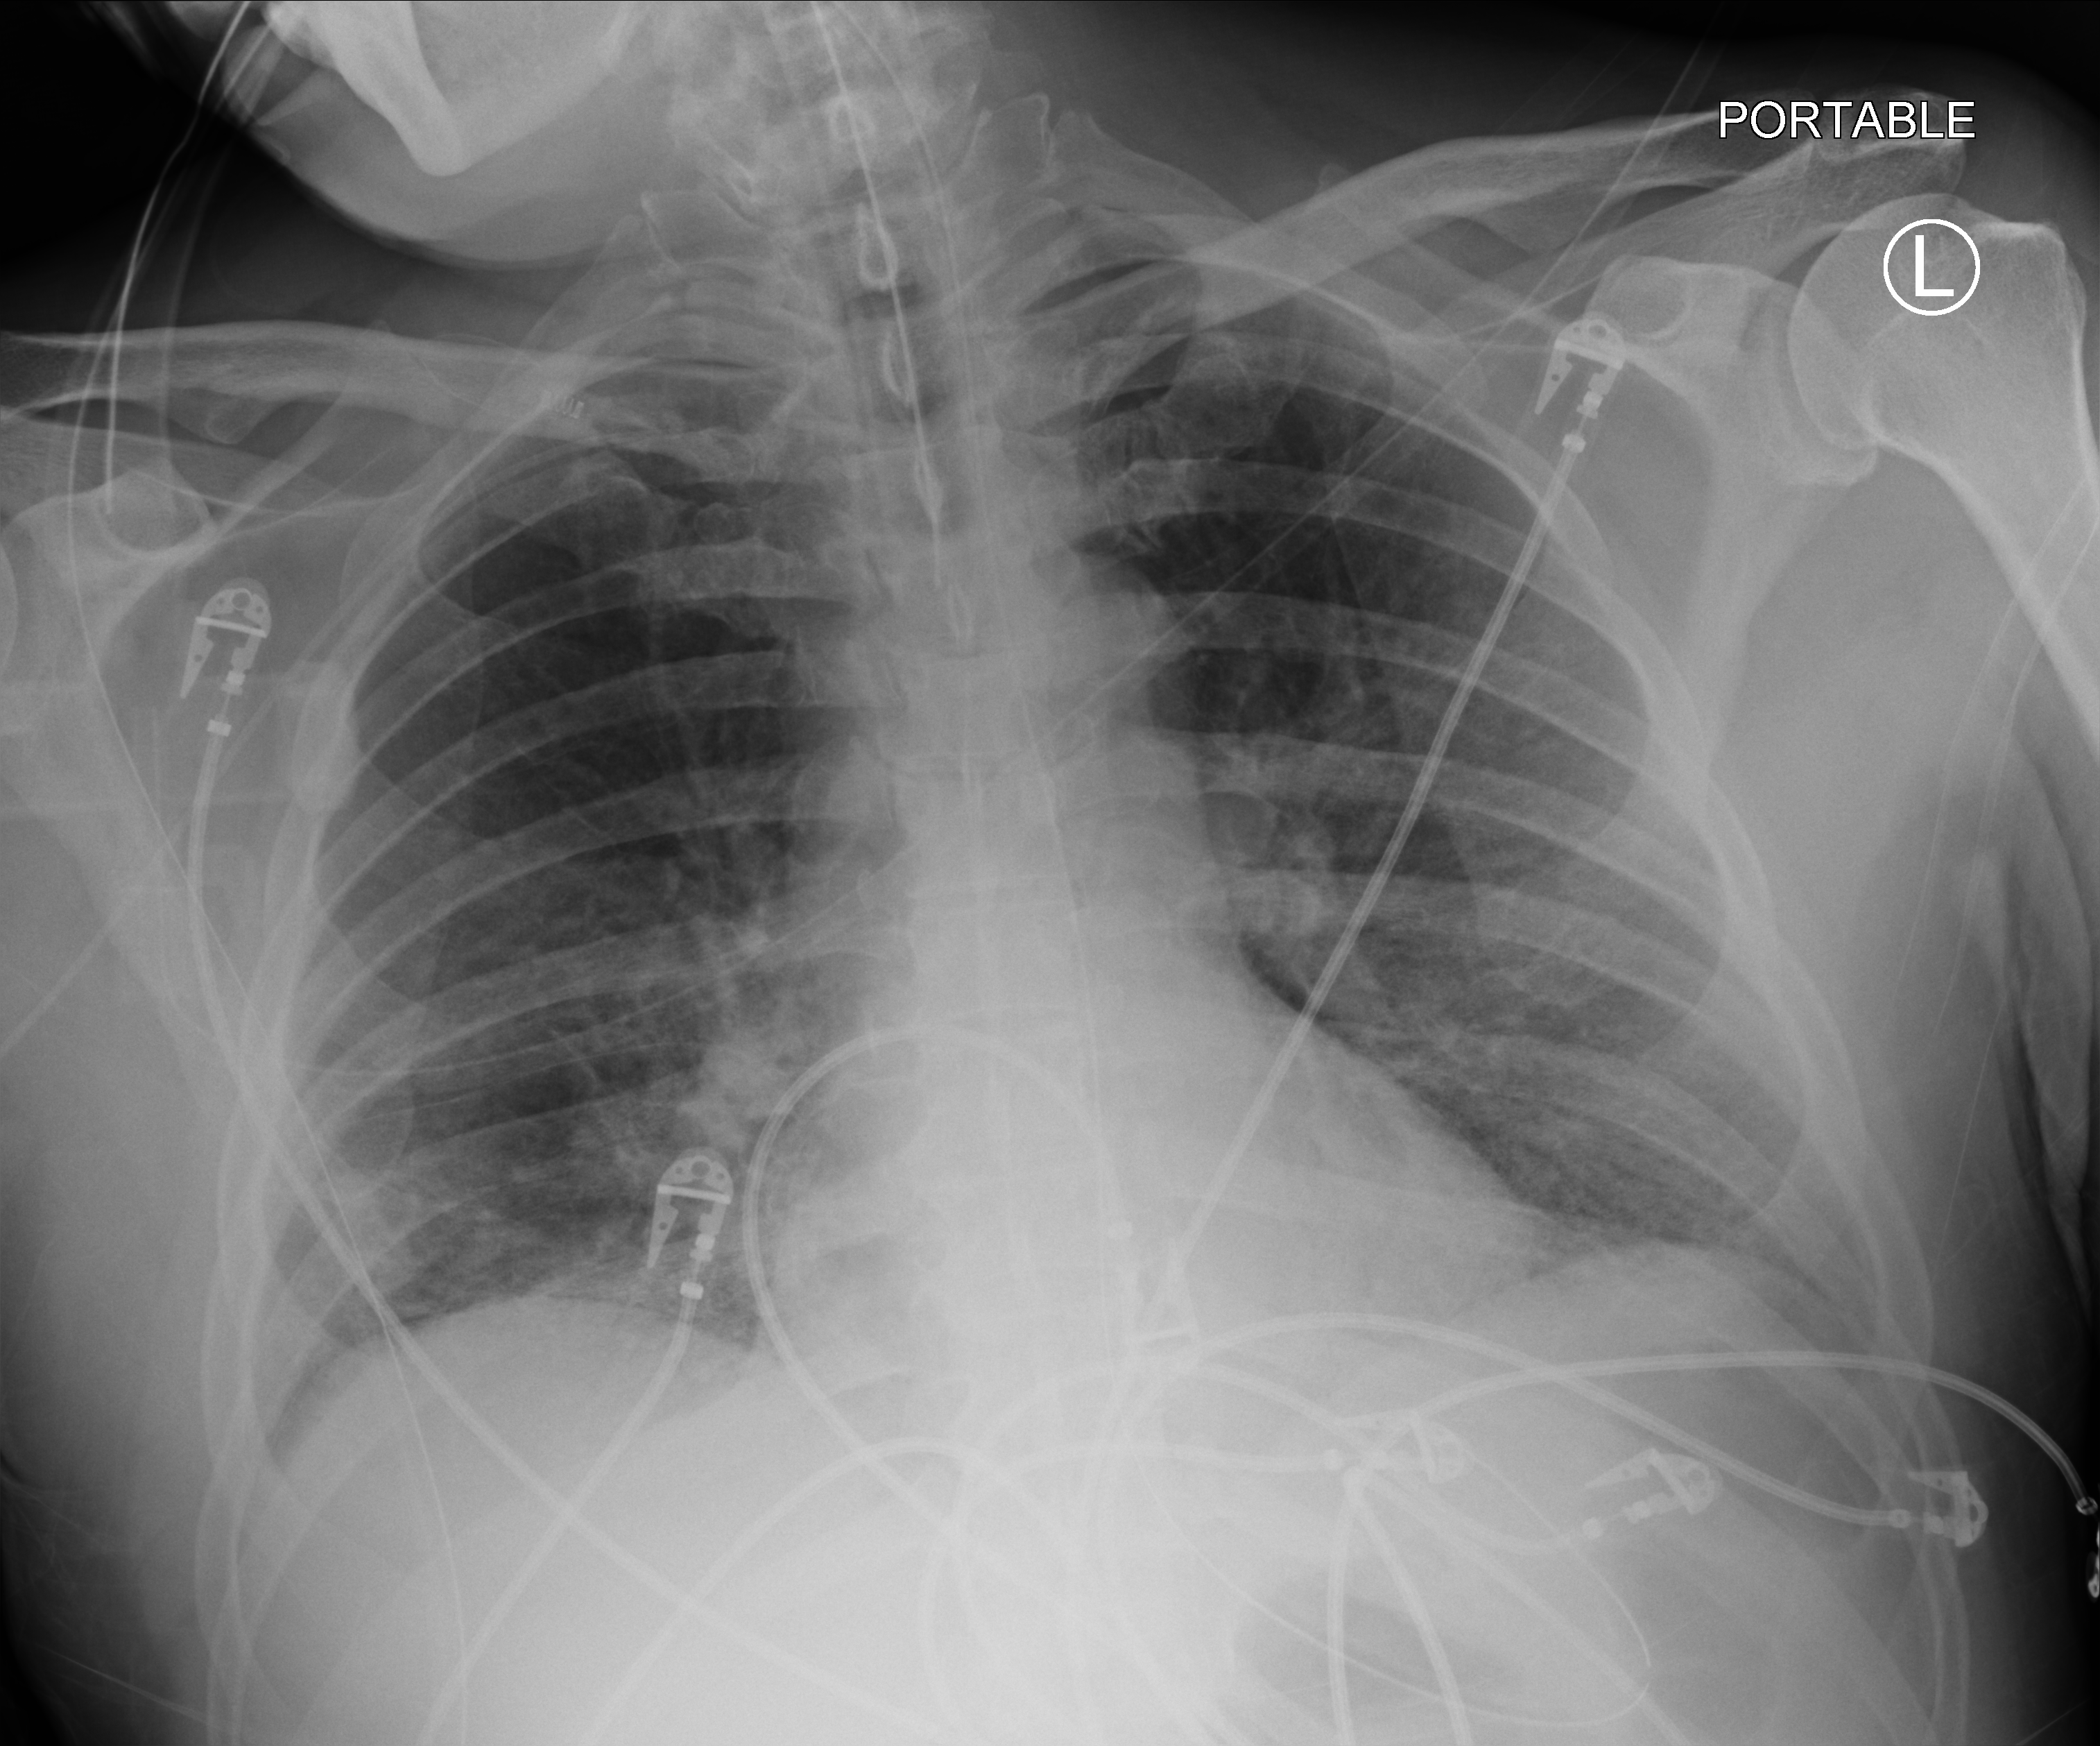
Bedside chest radiograph (computed radiography). Male patient hospitalised with COVID-19, age 60–74 years.
Admission-level facts for this patient (not findings on this image; timing relative to this image not recorded):
- smoking status (admission record): never
- admitted to intensive care during this hospital stay: yes
- mechanically ventilated during this hospital stay: yes